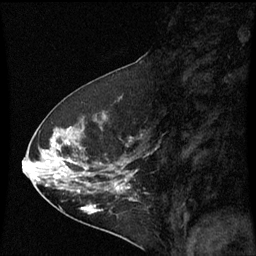
Breast MRI (dynamic contrast-enhanced), one sagittal slice. Slice 27 of 60 in the series (ordered by position). Dynamic contrast-enhanced series, image 2 of 3 at this slice position (ordered by acquisition). 1.5 T. TE 4.2 ms, TR 8.9 ms. 2 mm slice thickness. 256 × 256 image matrix, field of view 200 × 200 mm. Patient: female, 53 years. Case-level facts recorded for this patient, not image findings: setting: breast cancer imaged before/during neoadjuvant chemotherapy; receptor status: HR-positive, HER2-negative.
Structures marked on this image (semi-automatically segmented with operator editing):
- analysis volume of interest (the breast-tissue region the enhancement analysis was run in; not a lesion): bounding box [x1, y1, x2, y2] px = [32, 100, 143, 221]
- tumour enhancement mask (voxels above the 70 % enhancement threshold inside the analysis volume of interest): [52, 130, 133, 215]